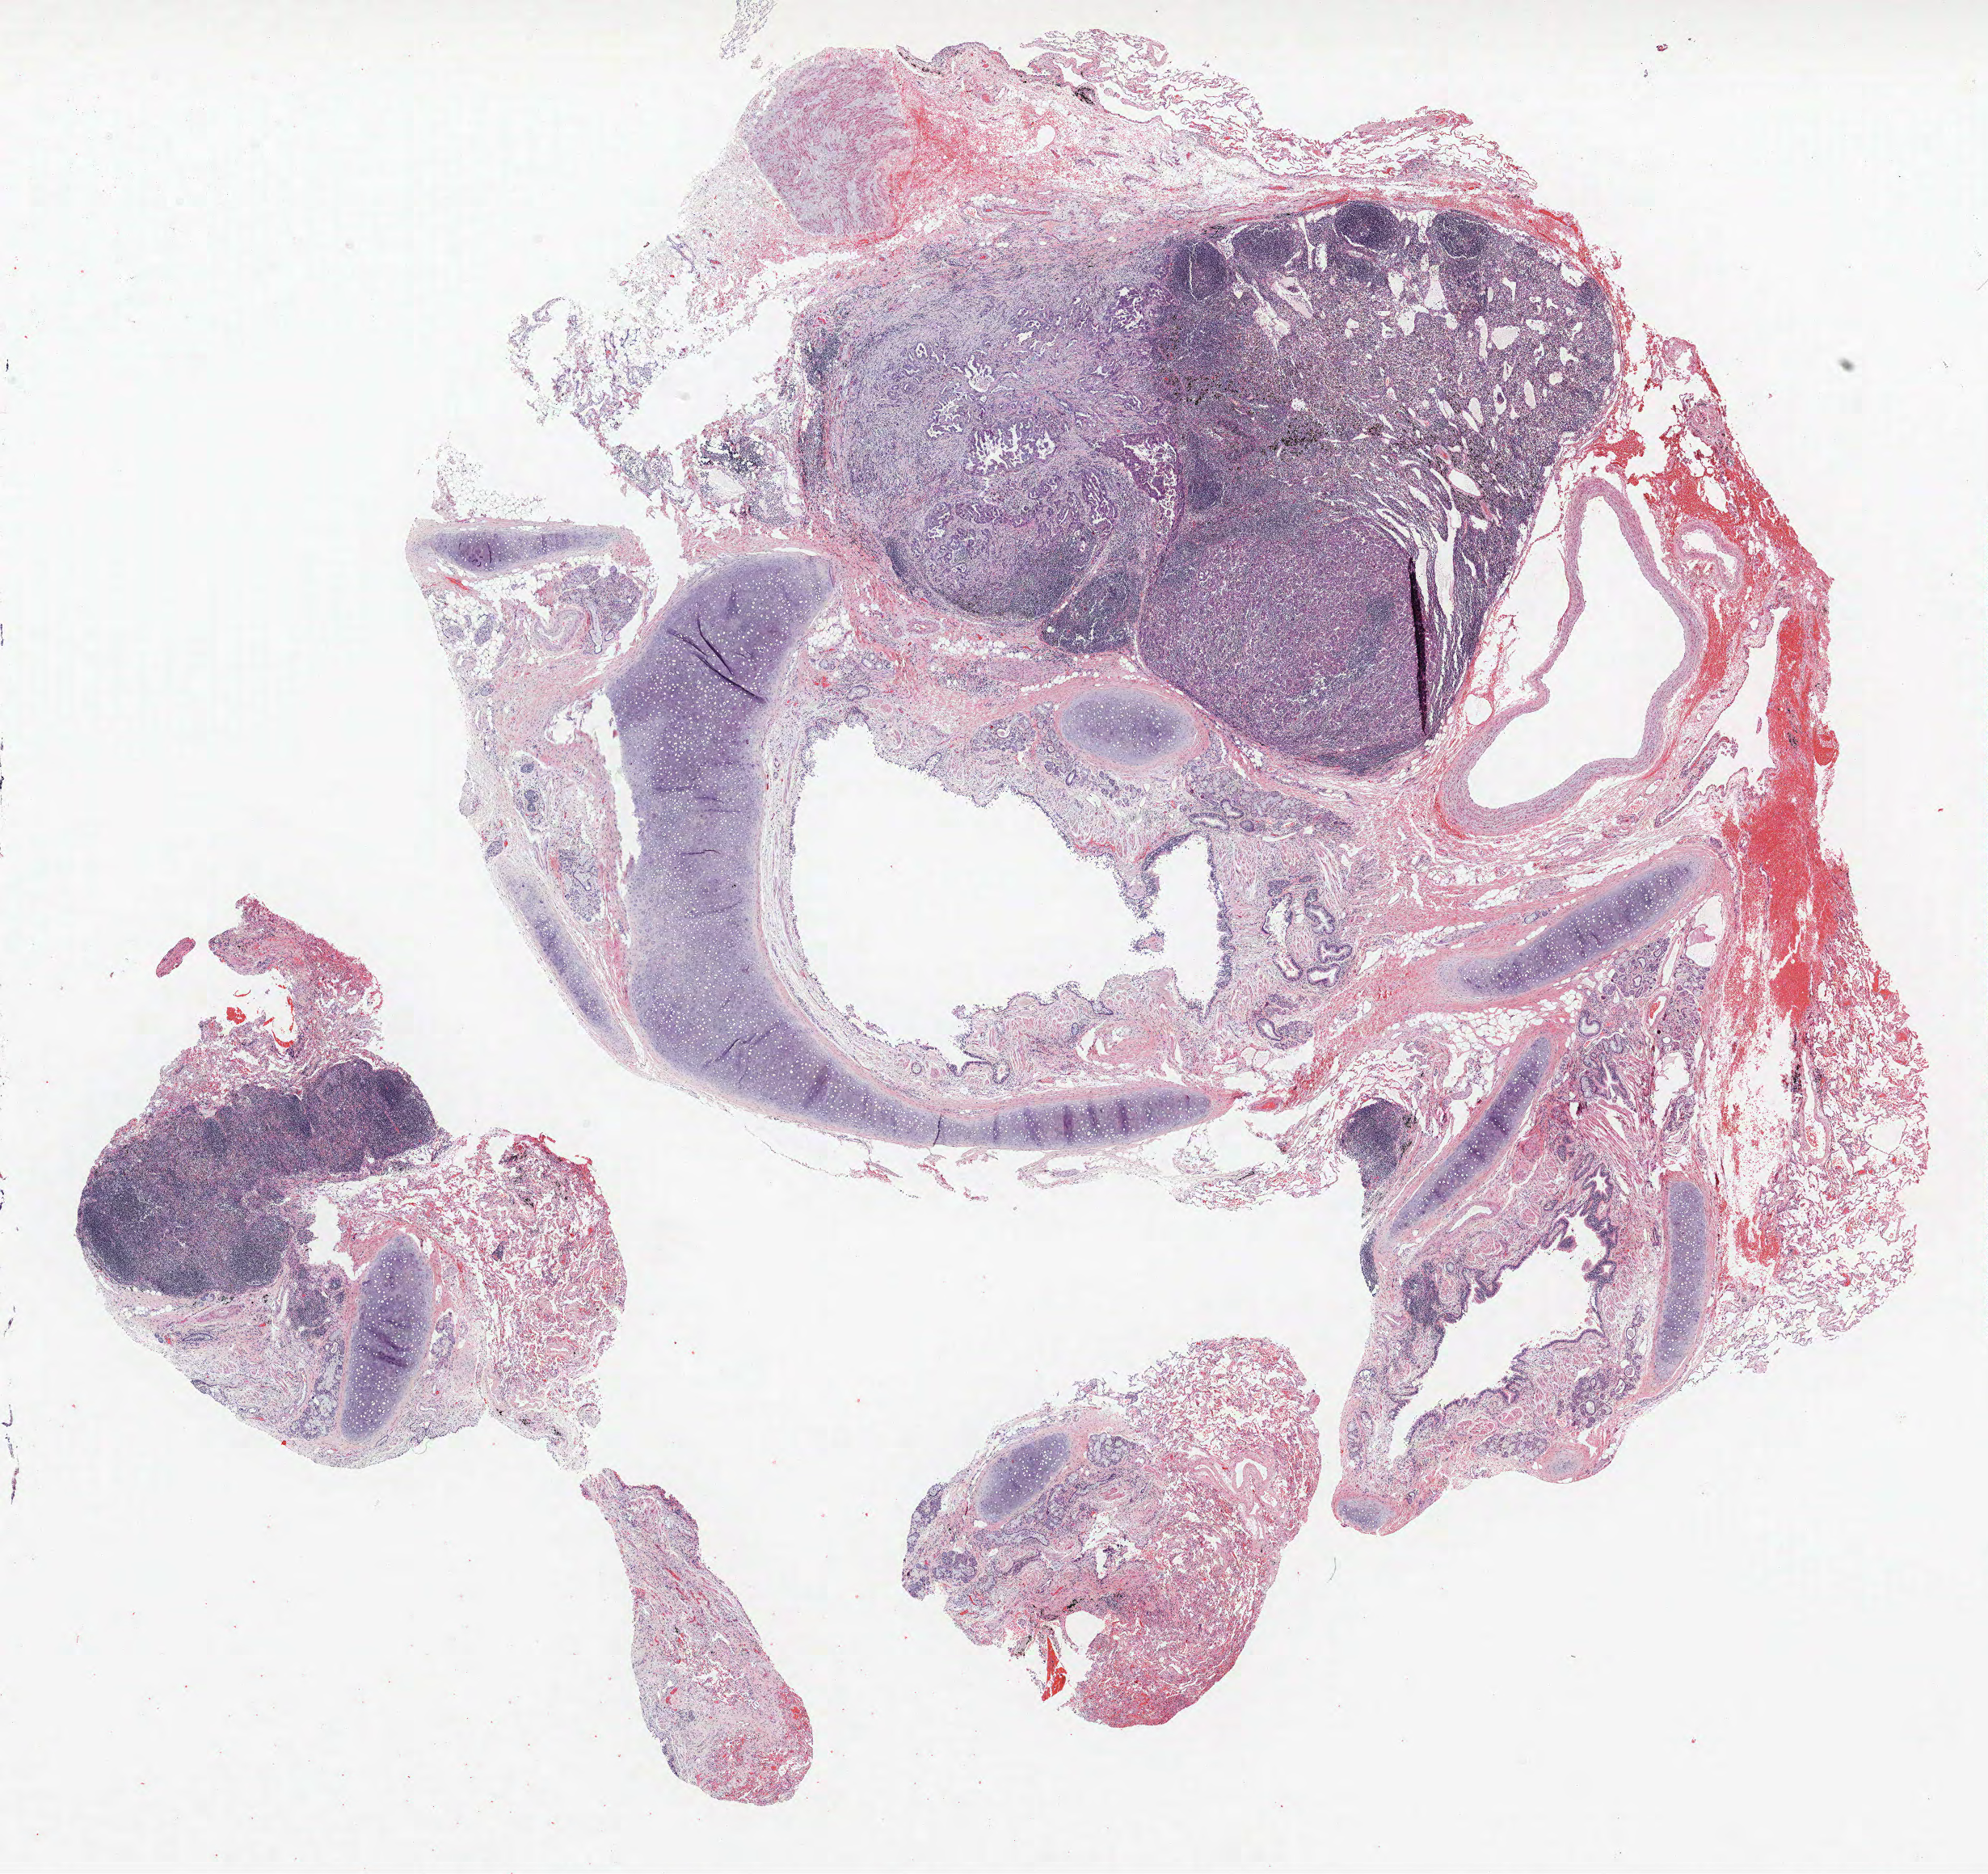
Whole-slide histology image, H&E — a low-resolution overview of the entire scanned area, about 19.7 x 18.6 mm (slide scanned at 40x); FFPE section; lung tissue. Male patient, aged 69 at enrolment. Grade: moderately differentiated (G2).
Participant's lung-cancer diagnosis: Adenocarcinoma, NOS (ICD-O-3 8140/3). Tumour size (pathology): 20 mm. Primary tumour location (clinical record): right upper lobe. Stage (AJCC 6th edition): IIA.